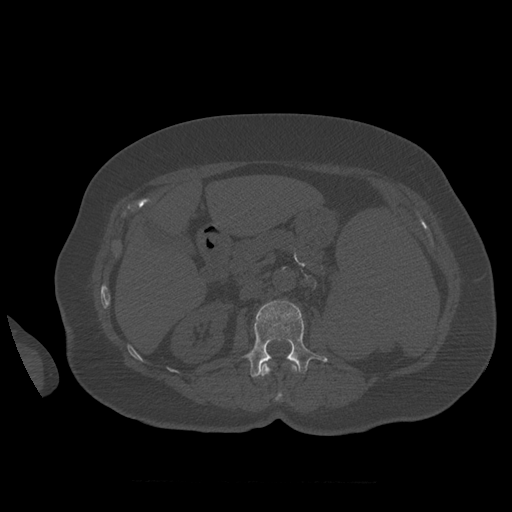
CT including the spine, one axial slice; slice 259 of 399 in the series (ordered by position); reconstruction kernel STANDARD; 120 kVp; bone window (W 1800 / L 400 HU); 1.25 mm slice thickness; 512 × 512 image matrix, field of view 404 × 404 mm. Patient age 81 years. From the clinical record (not read from this slice): primary cancer: renal; vertebrae with lytic lesions (as recorded): L1.
Outlined on this slice (semi-automatic segmentation, software-assisted and operator-edited):
- L1 vertebra: bounding box <260,364,297,400> (left, top, right, bottom; pixels)
- L2 vertebra: <239,301,328,378>